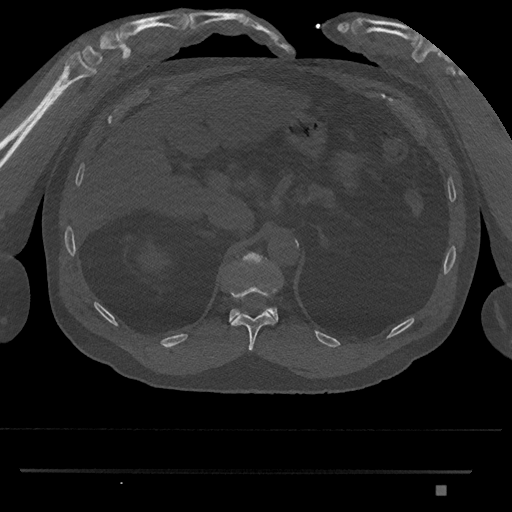
CT including the spine, one axial slice. Position 927 of 1134 along the scan axis. Bone window (W 1800 / L 400 HU). 512 × 512 image matrix, field of view 429 × 429 mm. Male patient, age 65 years. From the clinical record (not read from this slice): primary cancer: prostate.
Structures marked on this image (semi-automatically segmented with operator editing):
- T11 vertebra: bounding box <229,287,278,351> (left, top, right, bottom; pixels)
- T12 vertebra: <229,252,279,322>